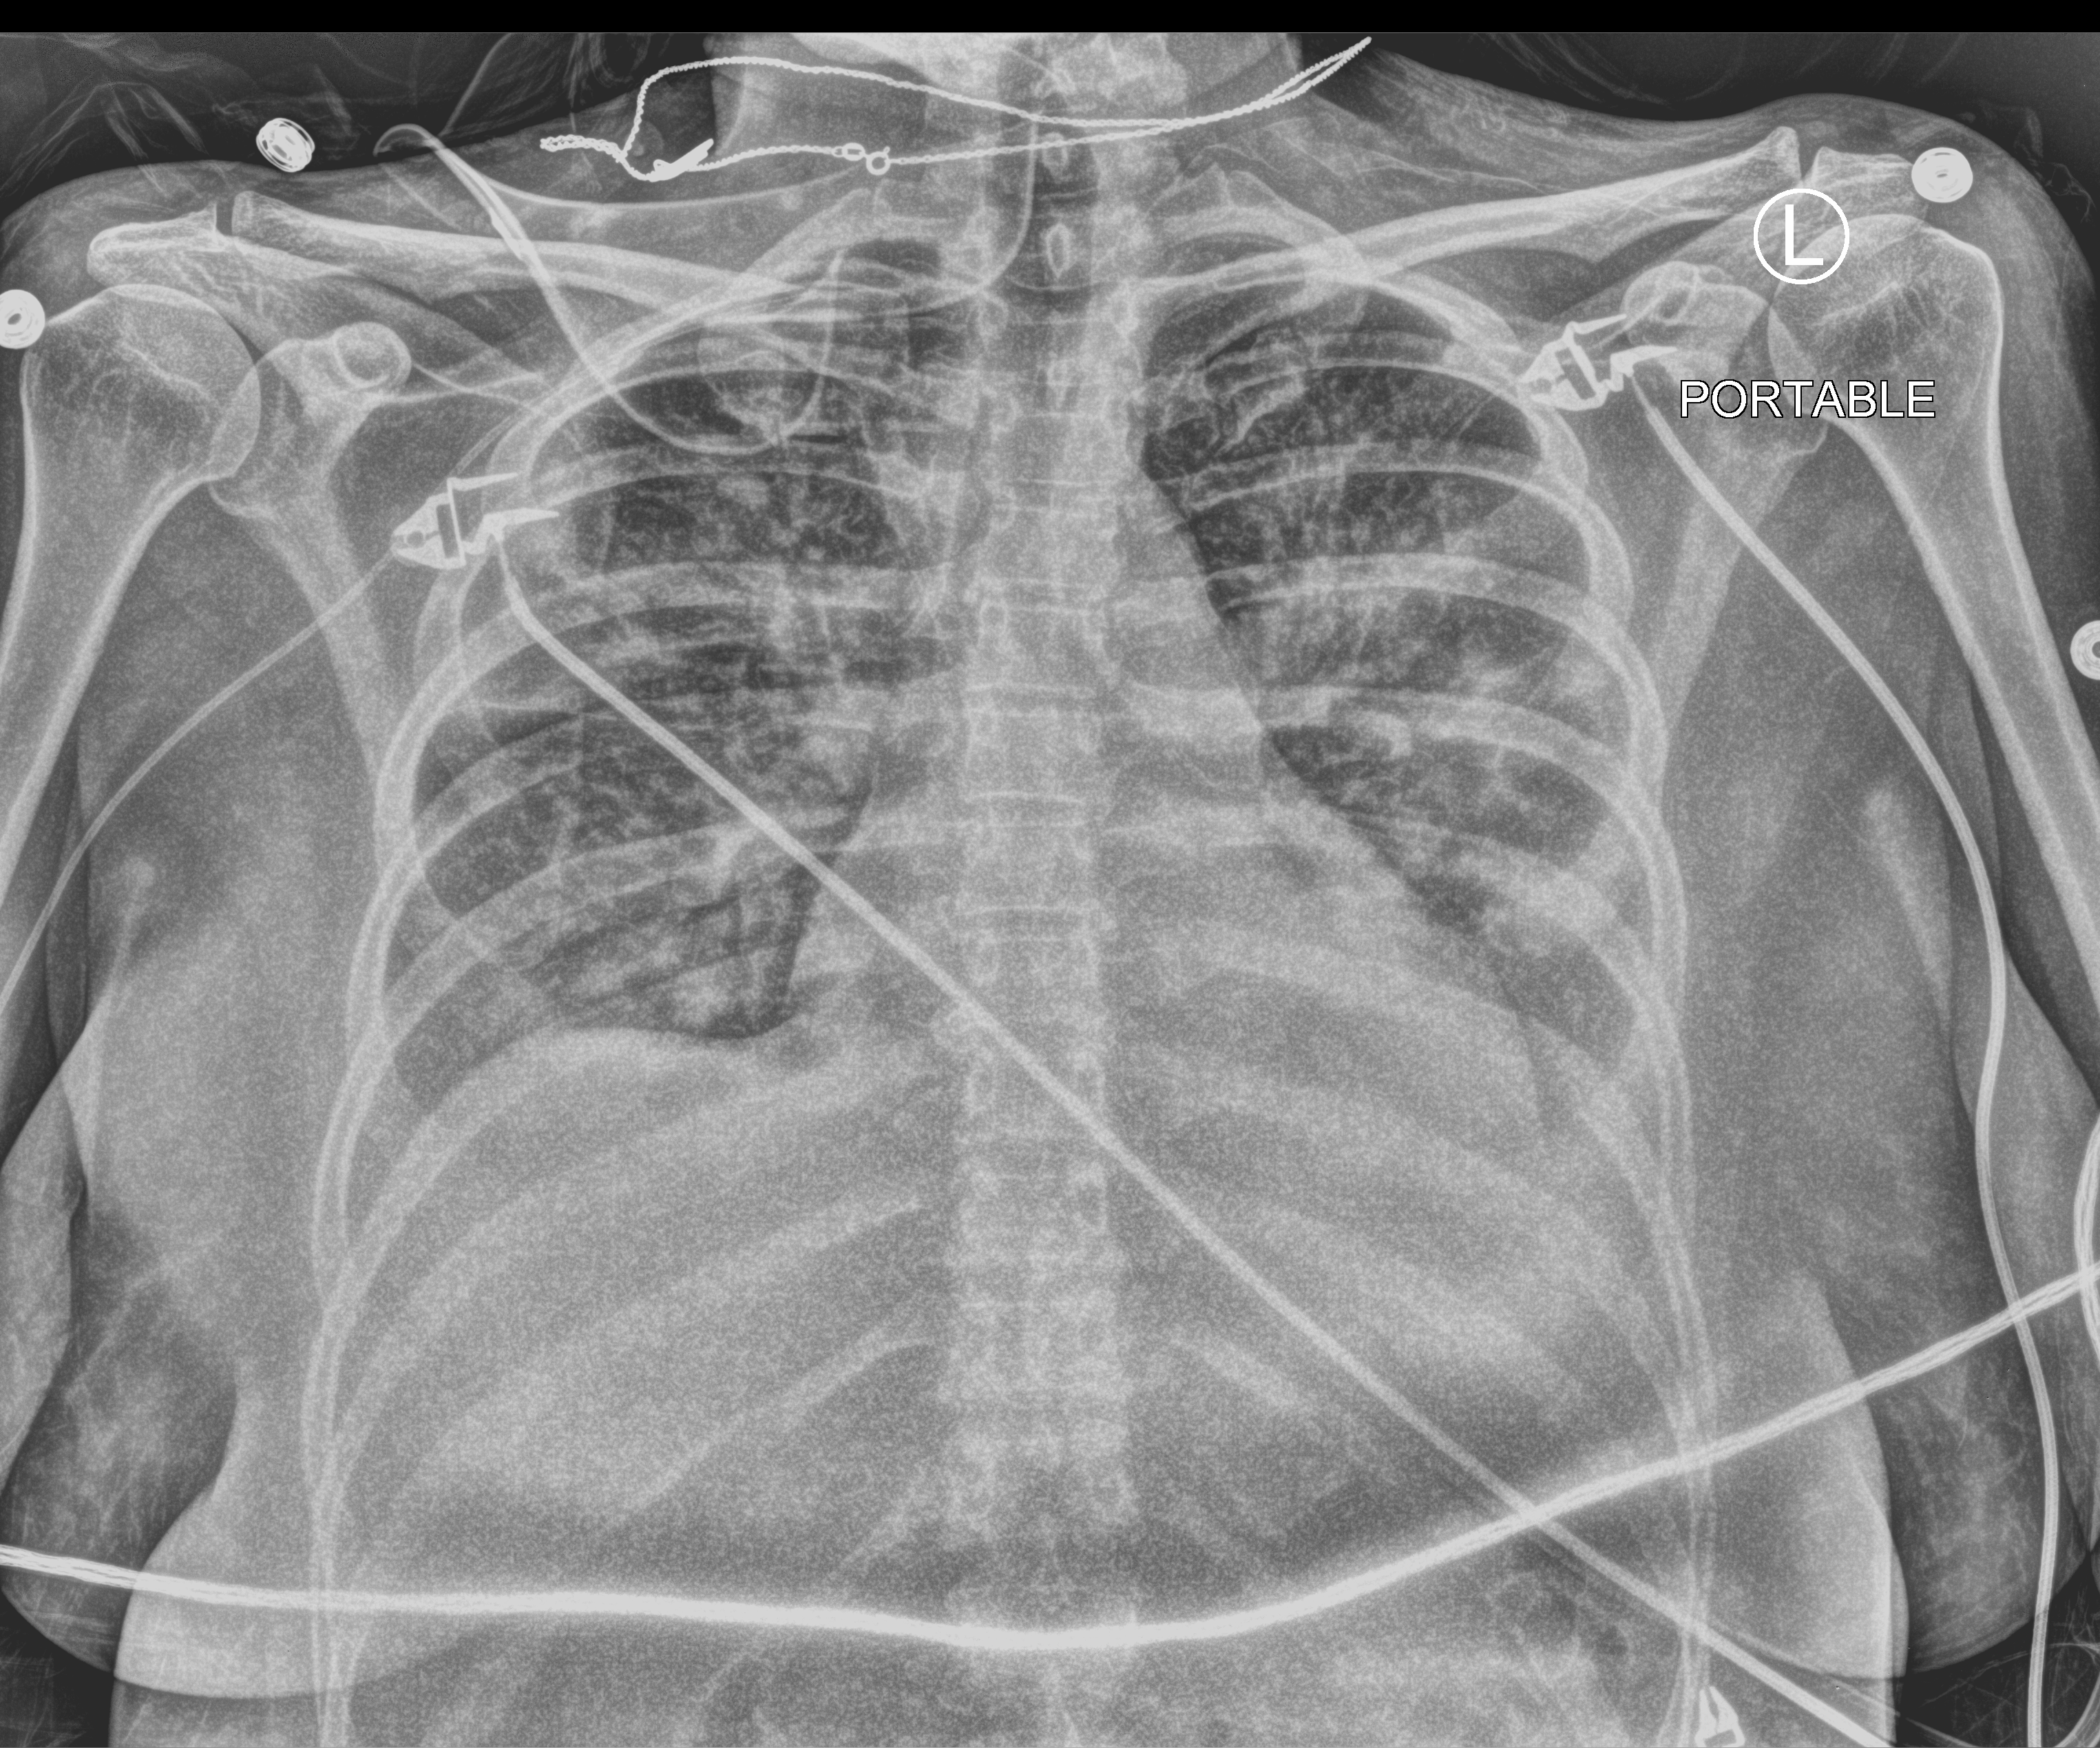
Portable chest radiograph, anteroposterior (AP) projection. Female patient hospitalised with COVID-19, age 18–59 years.
Hospital-stay facts (about this admission, not read from this image; timing relative to this image not recorded): mechanically ventilated during this hospital stay: no; admitted to intensive care during this hospital stay: no.